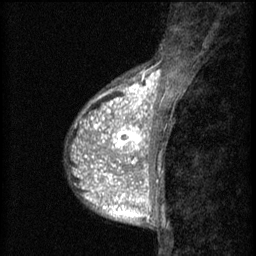
Breast MRI (dynamic contrast-enhanced), one sagittal slice. Slice 21 of 60 in the series (ordered by position). 3 images stored at this slice position (order not interpretable as contrast timing). 1.5 T. TE 4.2 ms, TR 8.2 ms. 2 mm slice thickness. 256 × 256 image matrix. Patient: female, 38 years.
Outlined on this slice (semi-automatic segmentation, software-assisted and operator-edited):
- analysis volume of interest (the breast-tissue region the enhancement analysis was run in; not a lesion): bounding box [x1, y1, x2, y2] px = [92, 112, 152, 171]
- tumour enhancement mask (voxels above the 70 % enhancement threshold inside the analysis volume of interest): [92, 112, 152, 171]